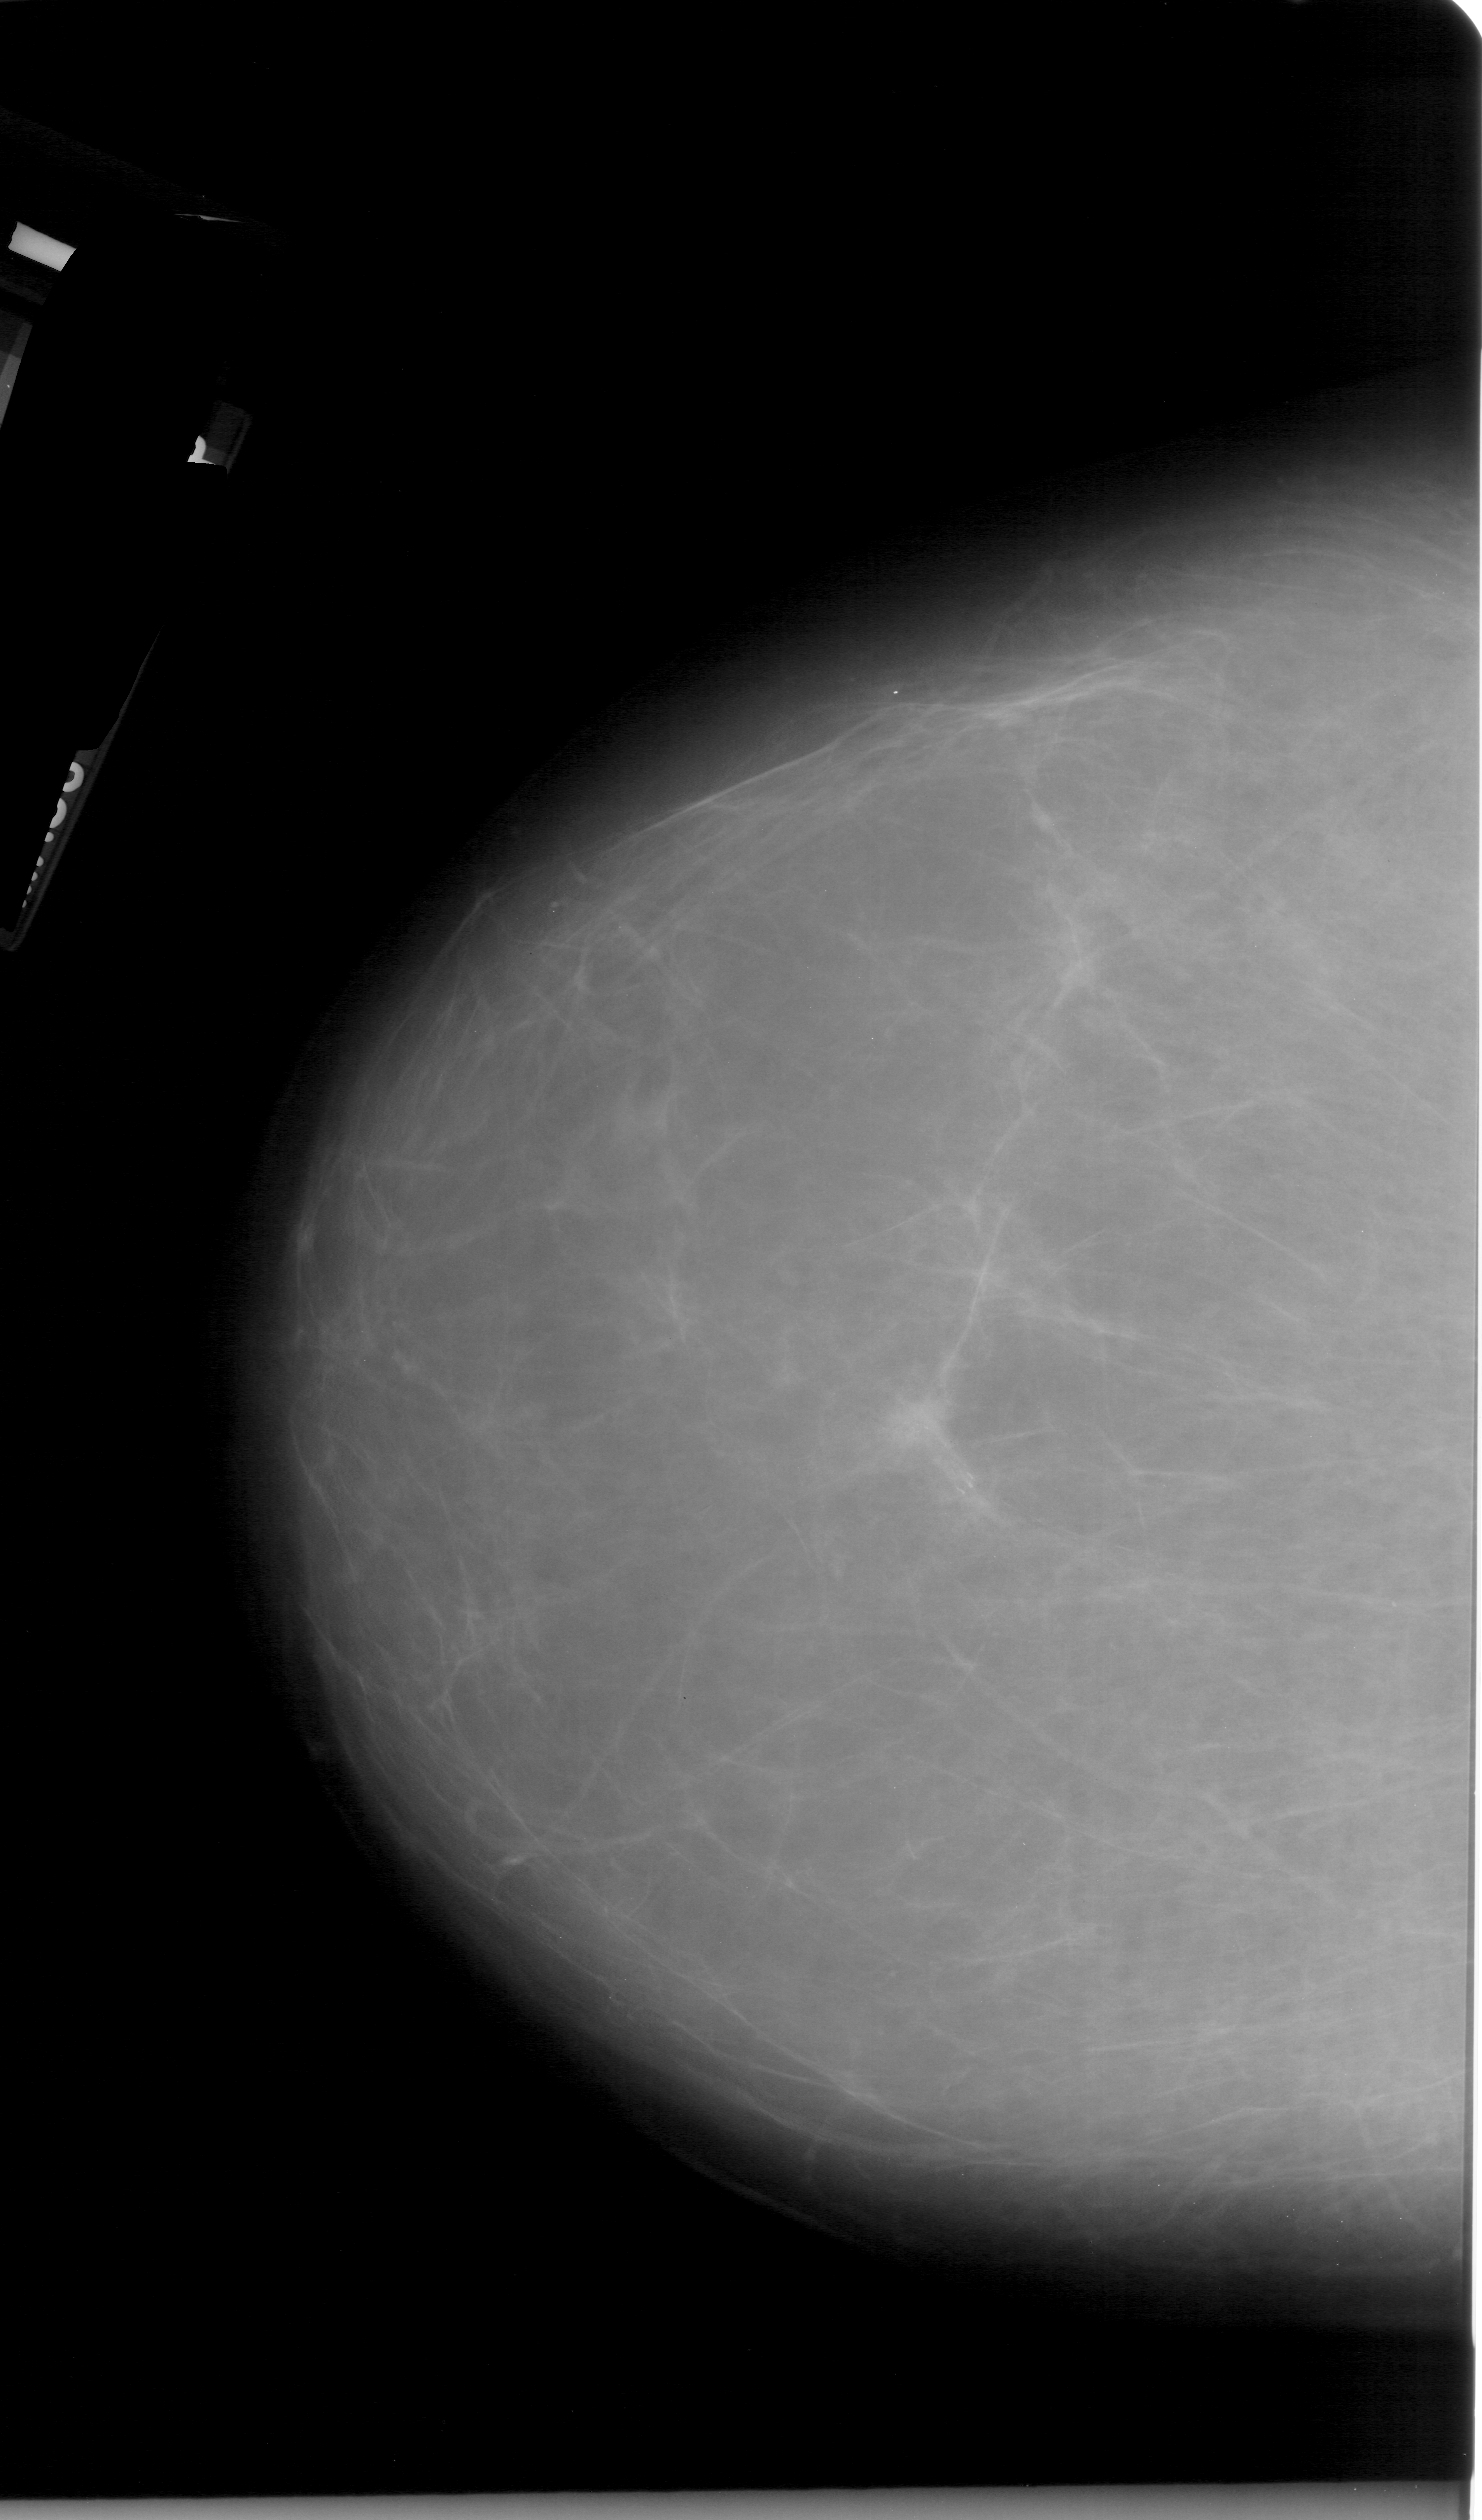
Digitized screen-film mammogram; left breast; CC view; BI-RADS breast density category 1 (scale 1–4).
Calcifications, morphology fine linear branching, distribution clustered; BI-RADS assessment category 4; pathology result (as recorded, not read from the image): malignant.